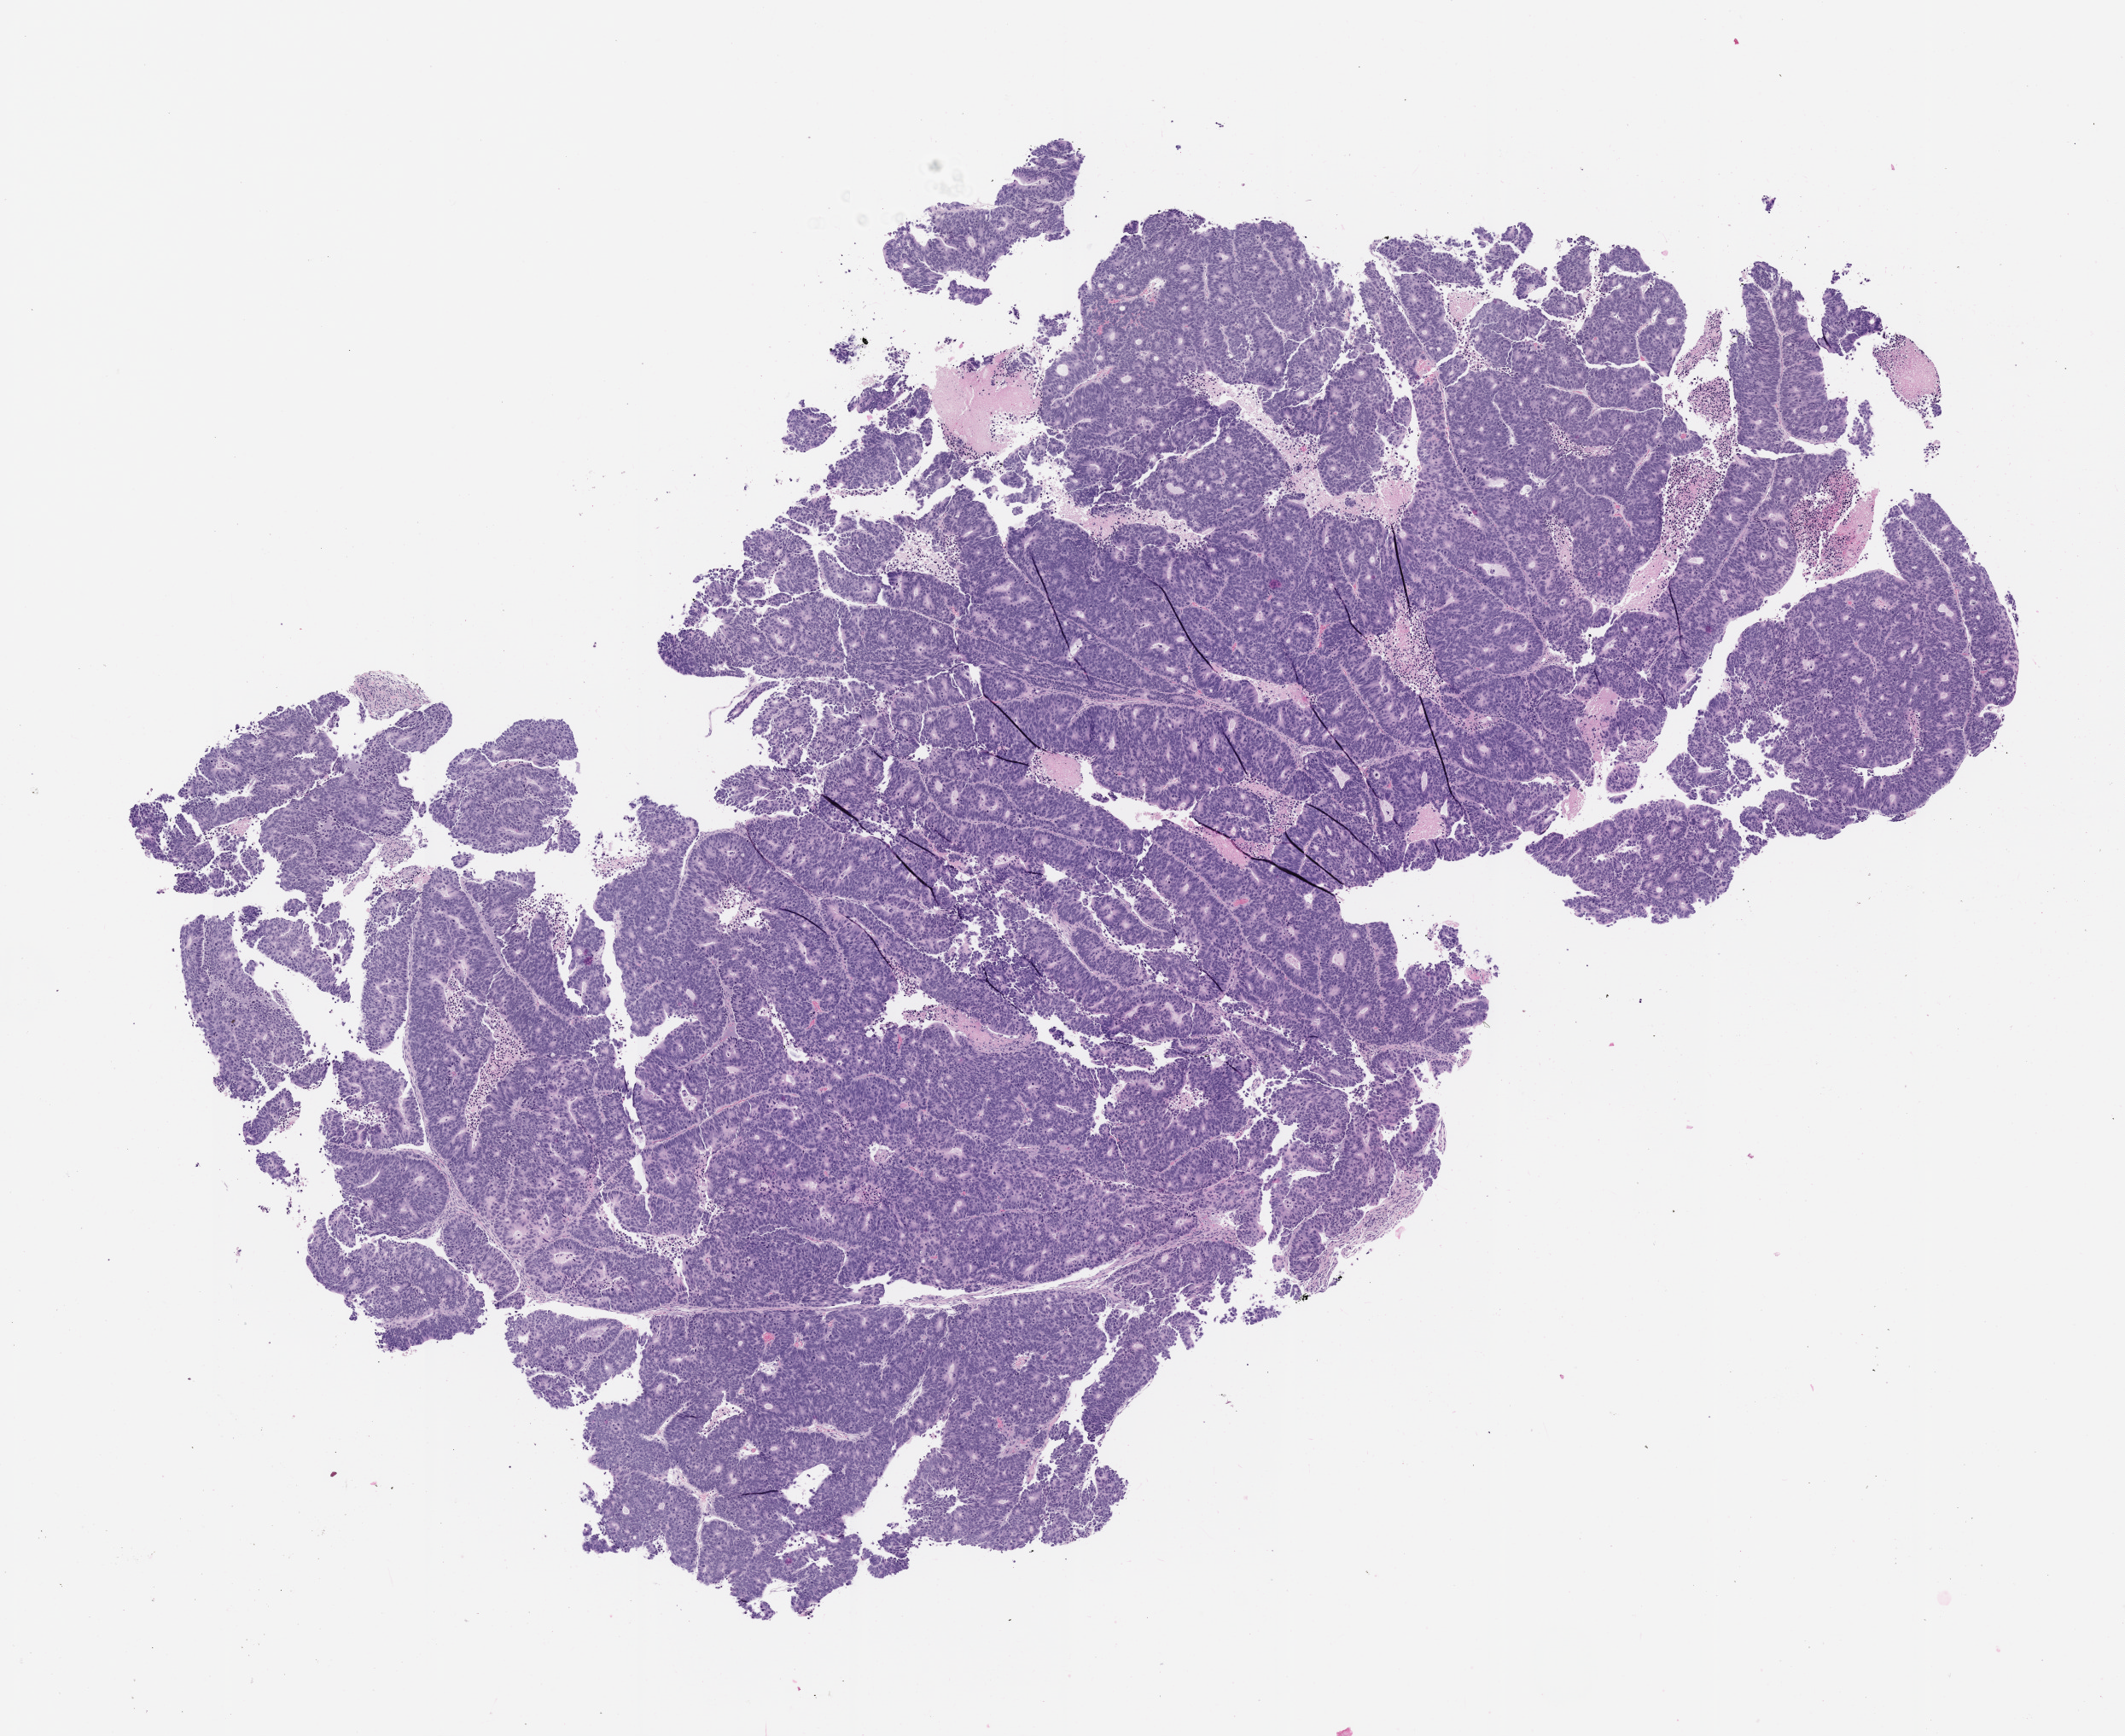
Haematoxylin and eosin whole-slide image of a patient-derived xenograft (PDX) tumor grown in a mouse, passage 0 — low-resolution overview of the scanned area, about 10.0 x 8.2 mm. FFPE section. Tumor site category: colon.
Originating patient diagnosis: Colon Adenocarcinoma.